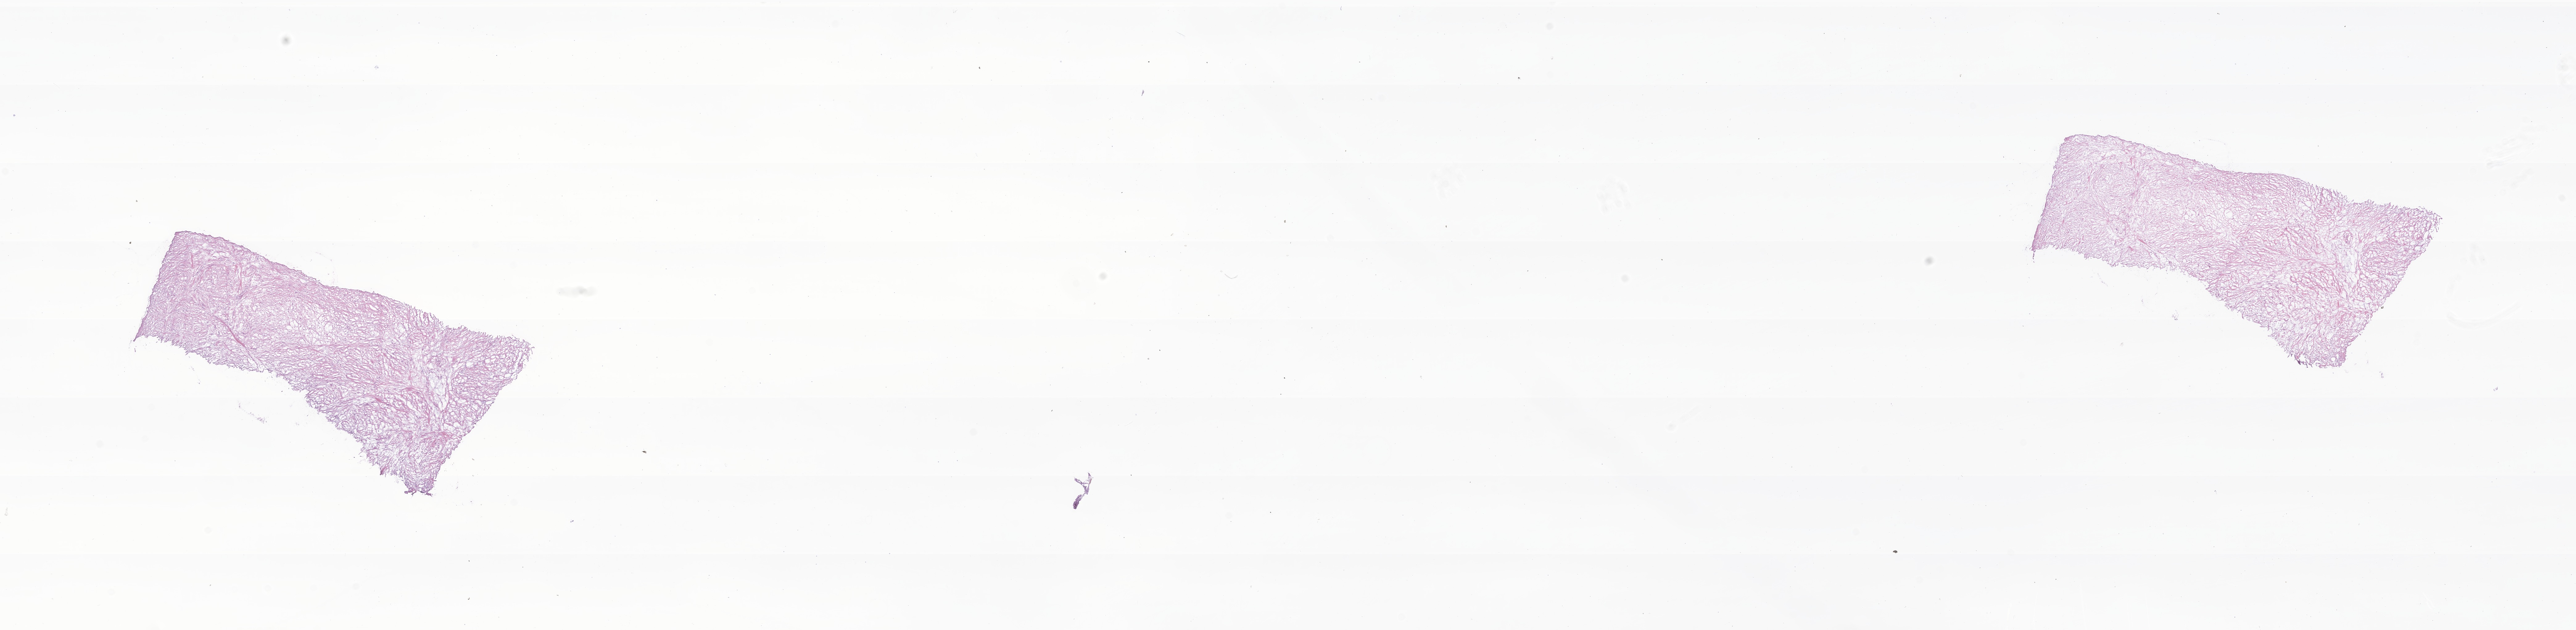
Digitized H&E-stained section of tumor tissue from the ileum — a low-resolution overview of the entire scanned area, about 35.2 x 8.6 mm. Cryosection (OCT / tissue freezing medium). Patient male; age 153 months (12 years 9 months).
- recorded diagnosis: Myofibroblastic tumor, NOS